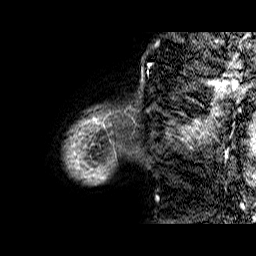
Breast MRI (dynamic contrast-enhanced), one sagittal slice; slice 1 of 60 in the series (ordered by position); dynamic contrast-enhanced series, time point 2 of 6 at this slice position (early post-contrast); 1.5 T; TE 6.5 ms, TR 32.9 ms; 4 mm slice thickness; 256 × 256 image matrix, field of view 200 × 200 mm. Female patient. Case-level facts recorded for this patient, not image findings: setting: breast cancer imaged before/during neoadjuvant chemotherapy; receptor status: HR-positive, HER2-negative.
Annotated regions visible in this slice (semi-automatic segmentation, software-assisted and operator-edited):
- analysis volume of interest (the breast-tissue region the enhancement analysis was run in; not a lesion): bounding box <64,74,176,185> (left, top, right, bottom; pixels)
- tumour enhancement mask (voxels above the 100 % enhancement threshold inside the analysis volume of interest): <85,122,106,166>